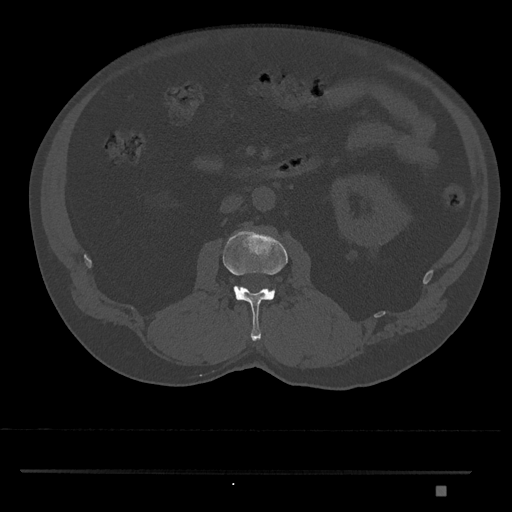
CT including the spine, one axial slice; slice 741 of 1134 in the series (ordered by position); reconstruction kernel Br40s/3; 120 kVp; bone window (W 1800 / L 400 HU); 0.5 mm slice thickness; 512 × 512 image matrix, field of view 429 × 429 mm. Patient: male, 65 years. Case-level facts recorded for this patient, not image findings: primary cancer: prostate.
Structures marked on this image (semi-automatic segmentation, software-assisted and operator-edited):
- L2 vertebra: bounding box (x1, y1, x2, y2) in pixels: (222, 229, 288, 341)